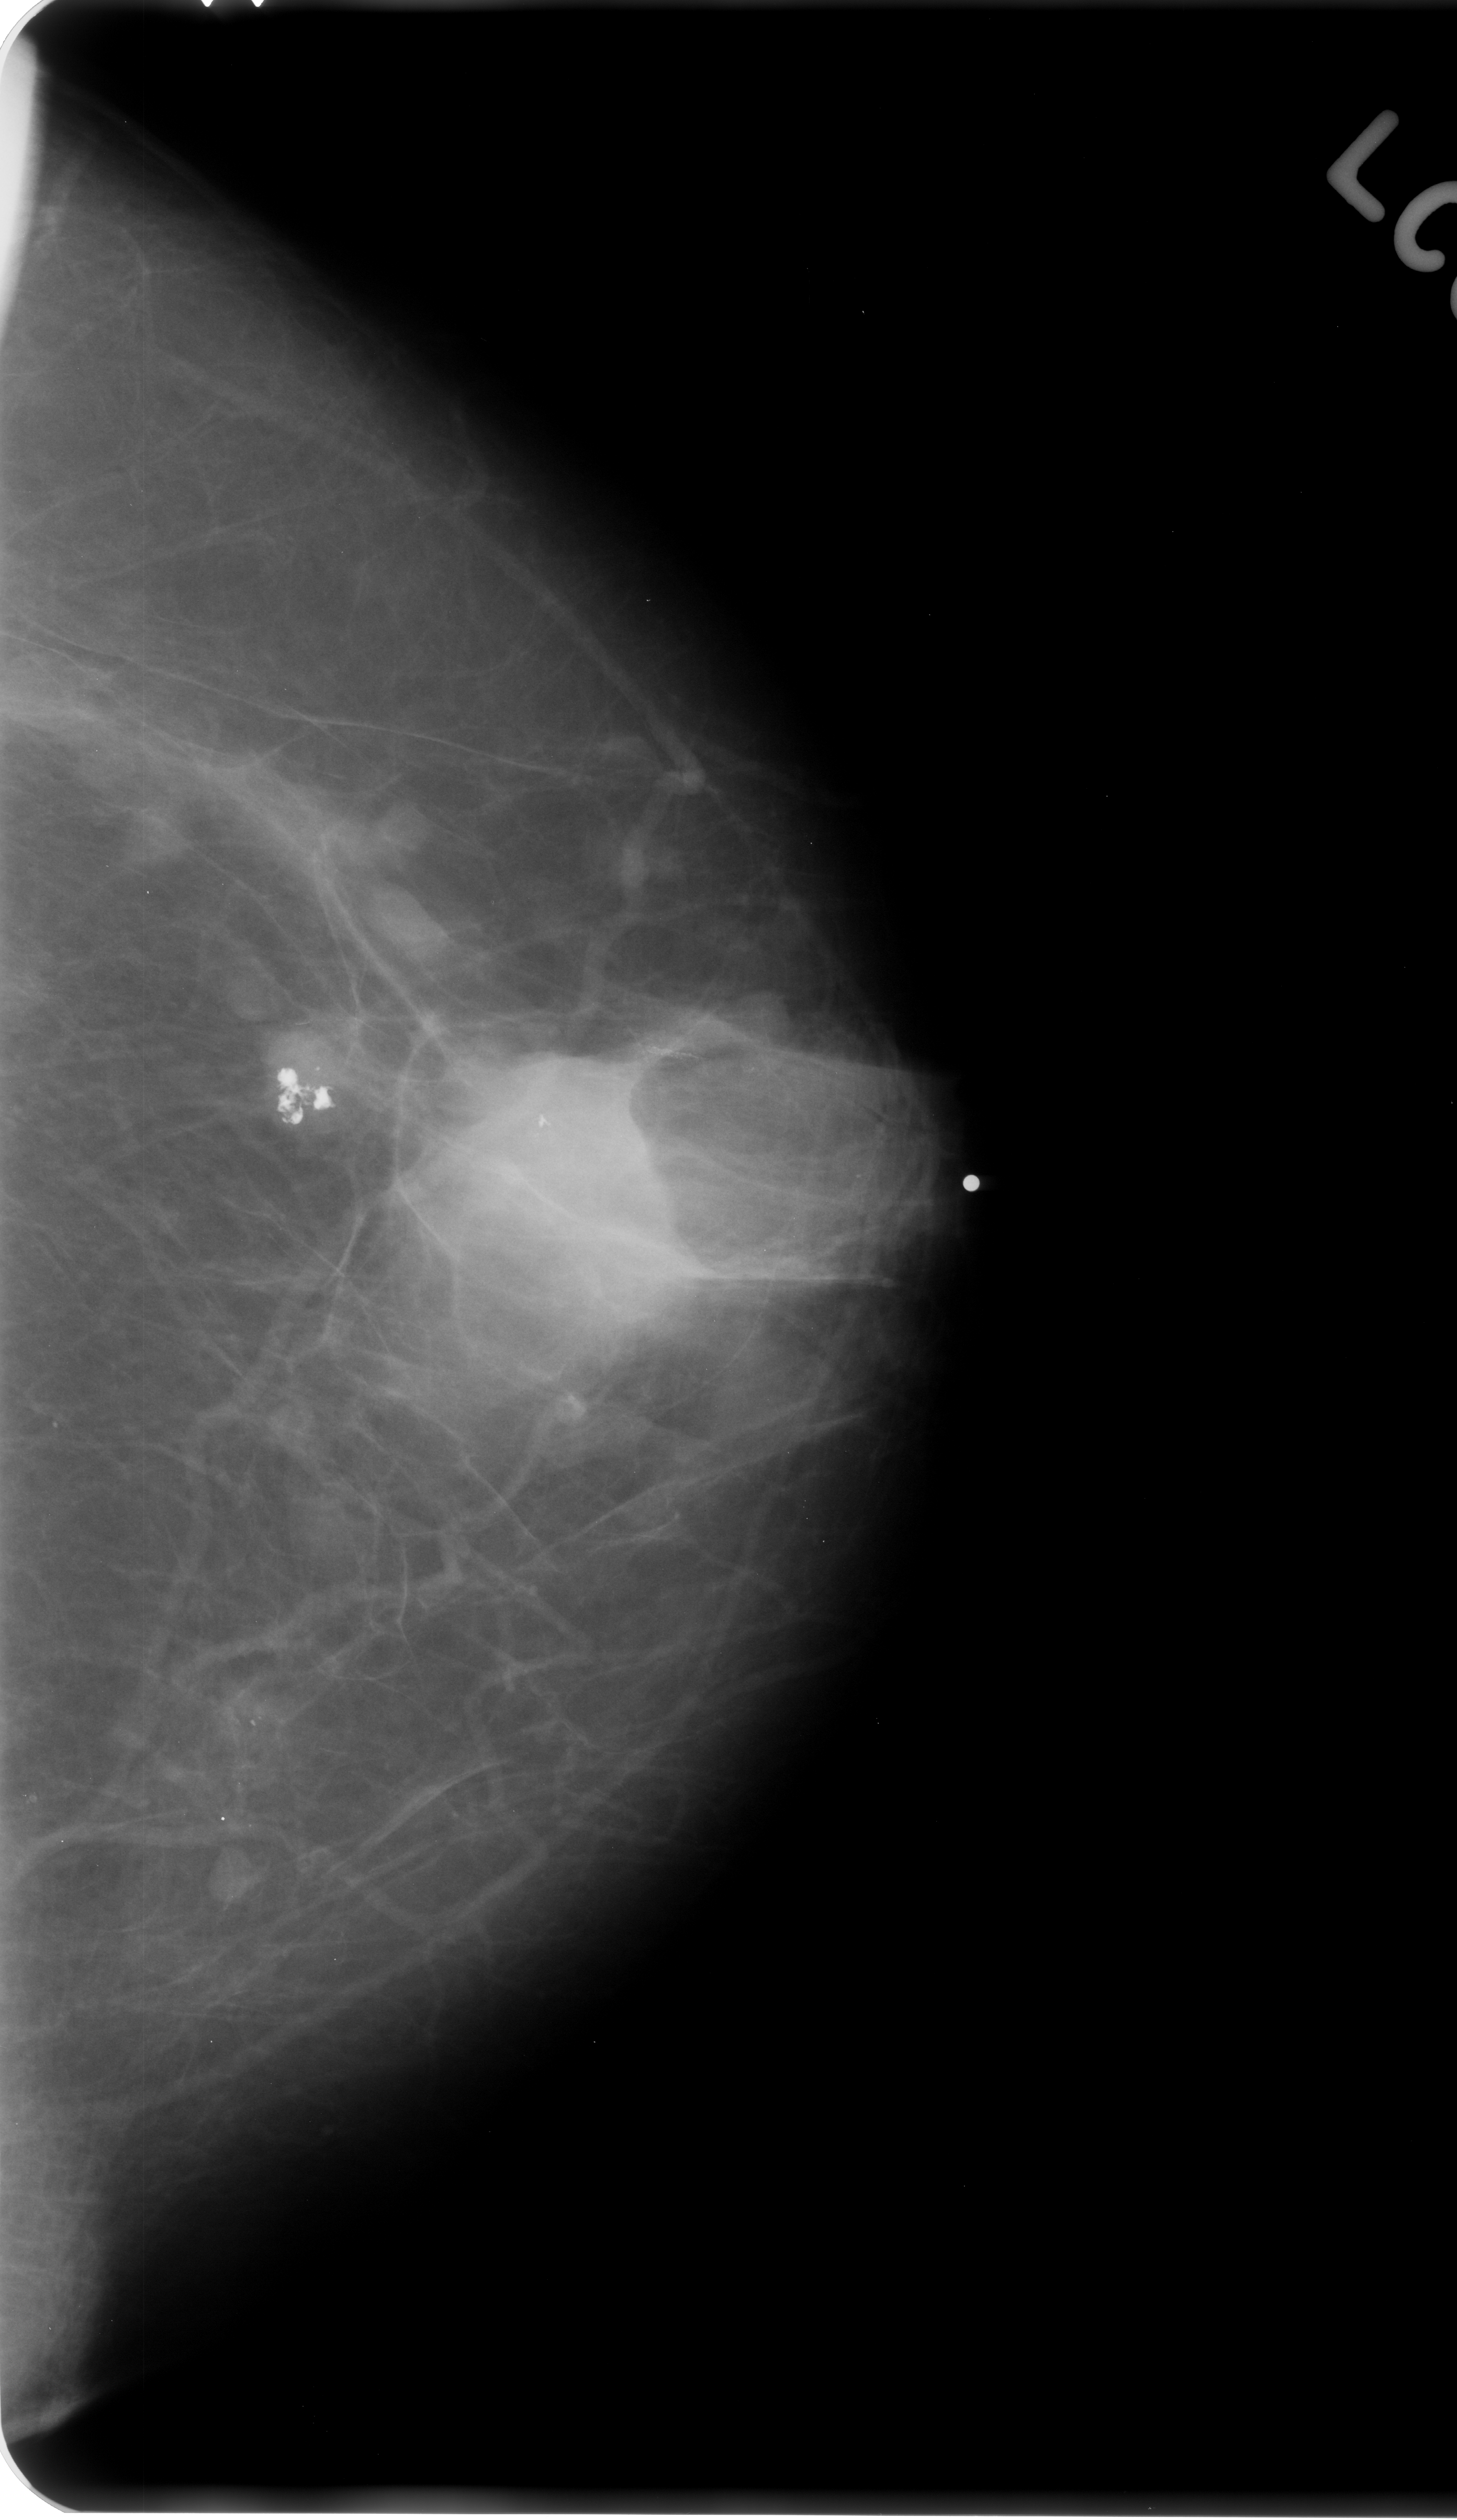
Scanned film-screen mammogram. Left breast. CC view. Breast composition: scattered fibroglandular densities (BI-RADS density category 2 of 4). 1457 × 2520 image matrix.
Expert-marked regions of interest on this film, with their recorded descriptors:
- mass, shape irregular, margins ill defined; BI-RADS assessment category 4; subtlety rating 3 on a 1 (subtle) to 5 (obvious) scale; pathology result (as recorded, not read from the image): malignant: bounding box (x1, y1, x2, y2) in pixels: (433, 1044, 707, 1314)